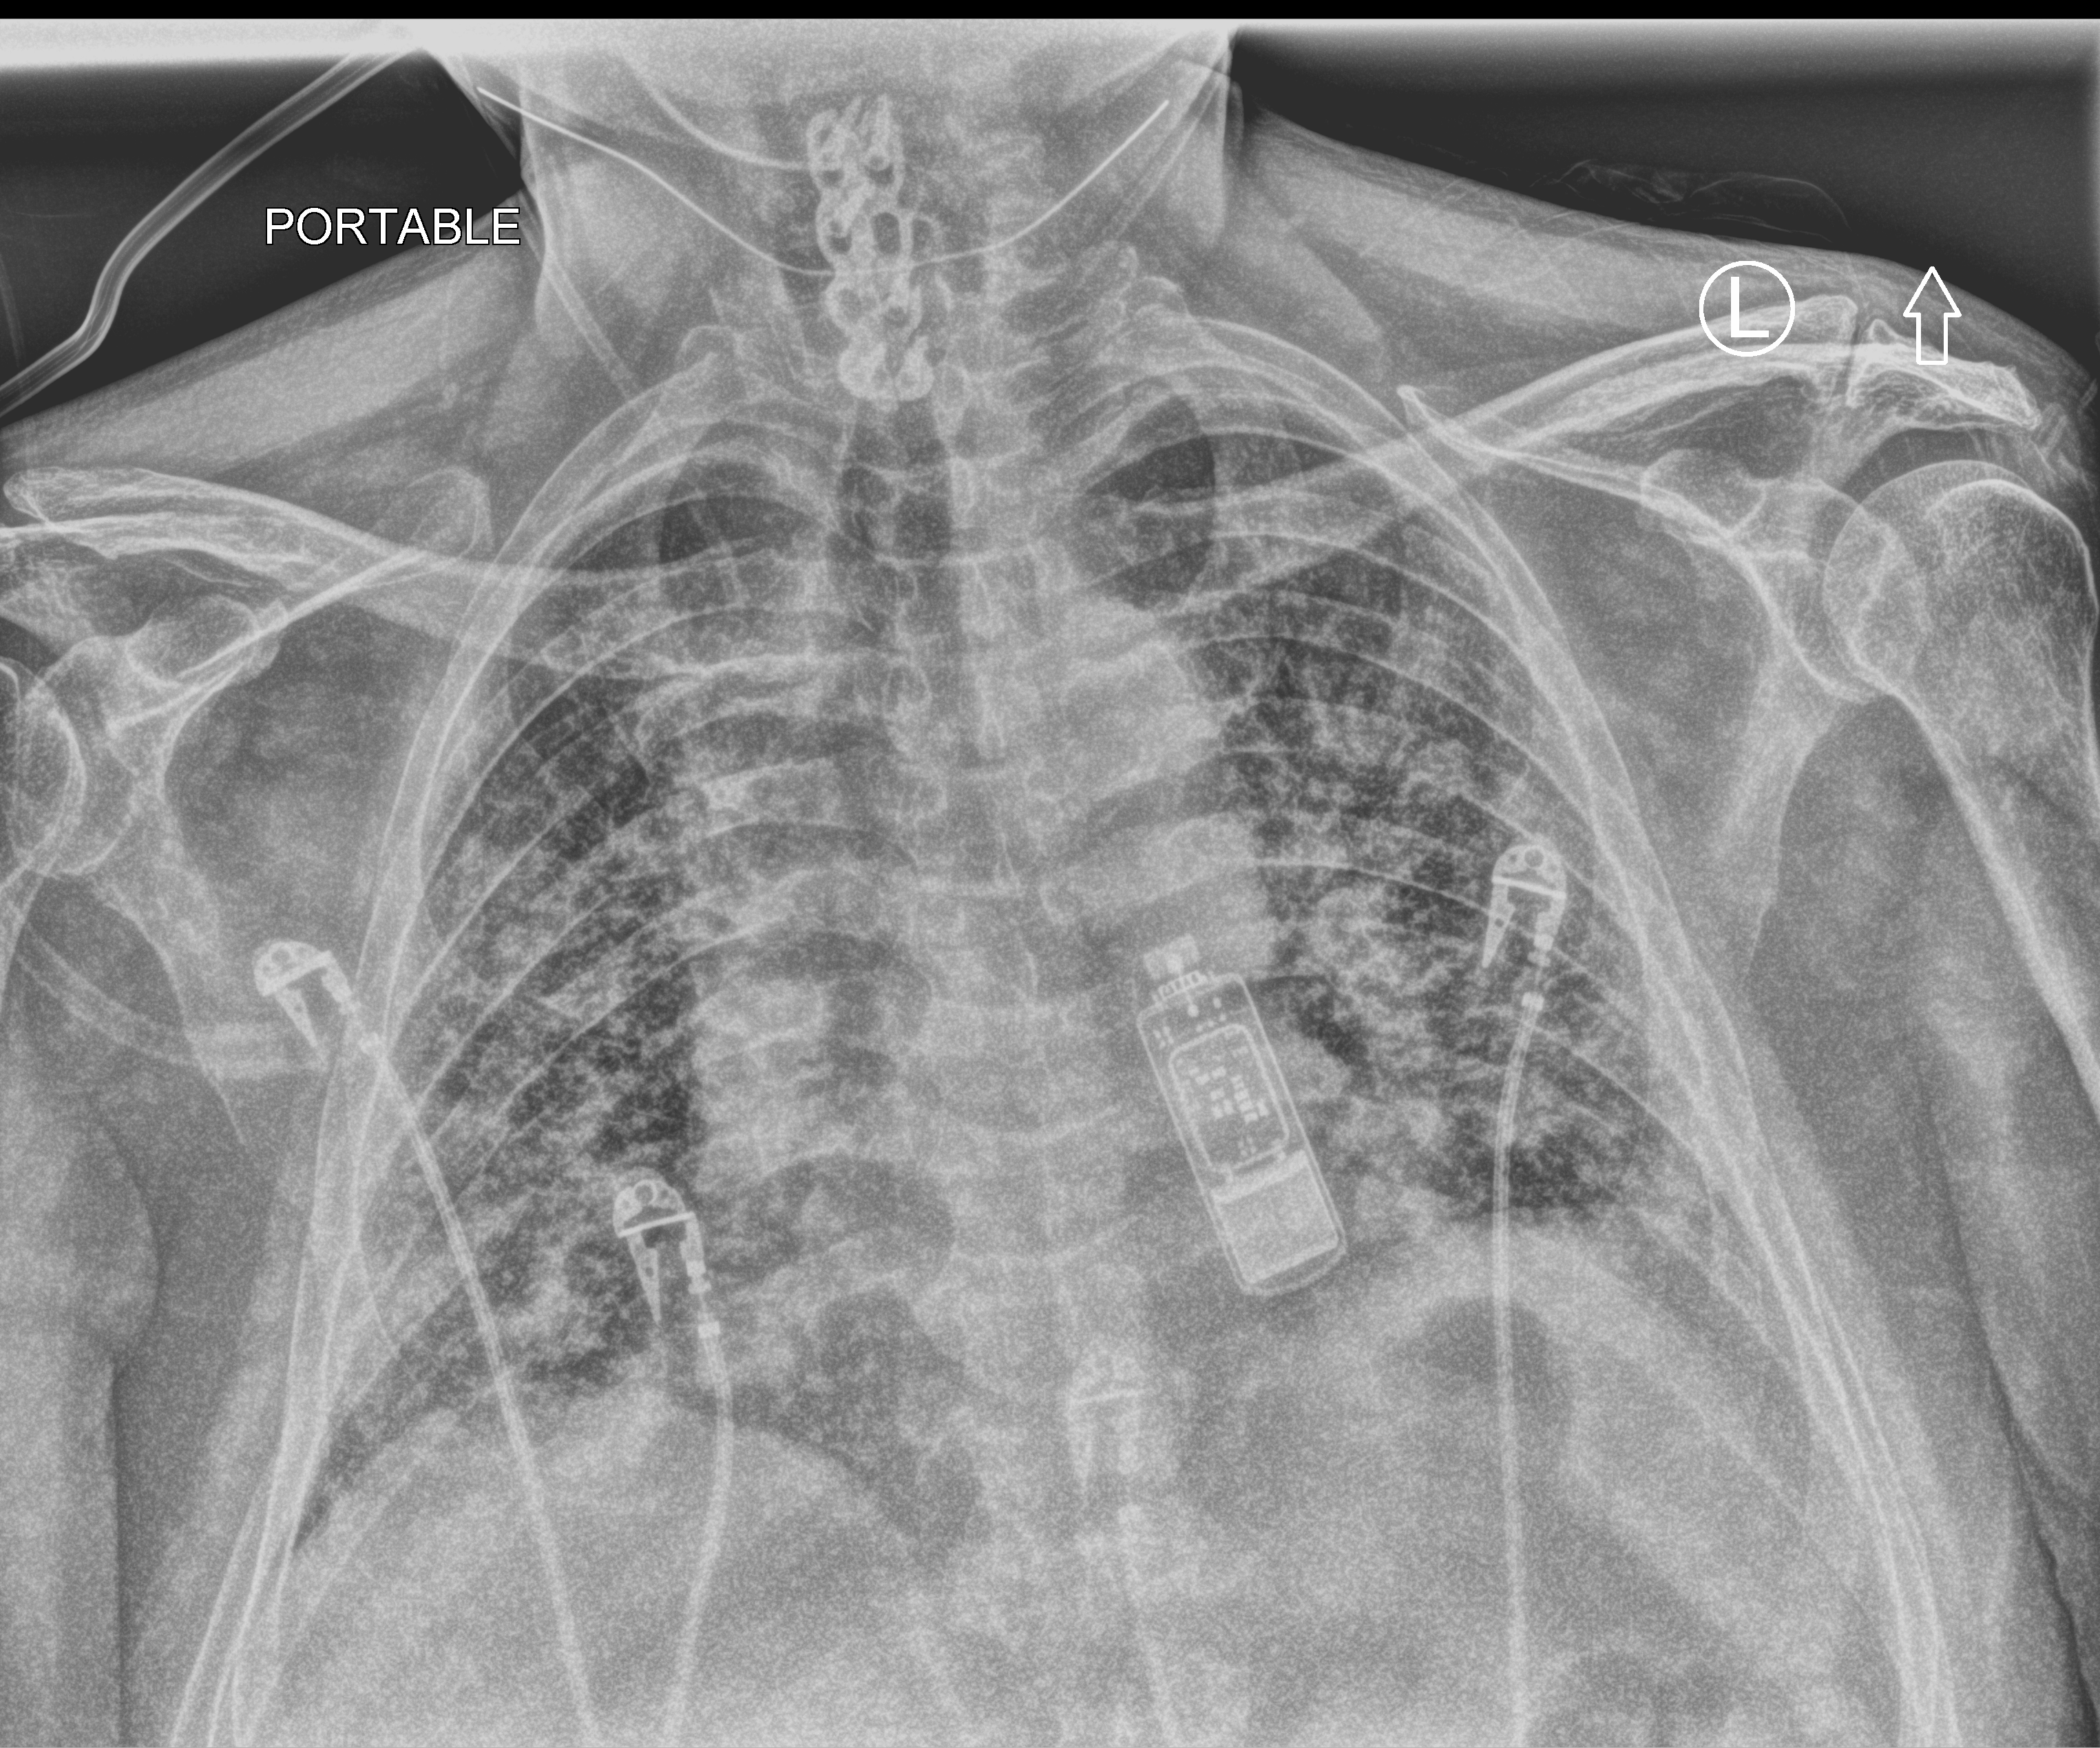
Chest X-ray (portable); anteroposterior (AP) projection. Patient hospitalised with COVID-19; male, aged 60–74 years.
Hospital-stay facts (about this admission, not read from this image; timing relative to this image not recorded):
- mechanically ventilated during this hospital stay: yes